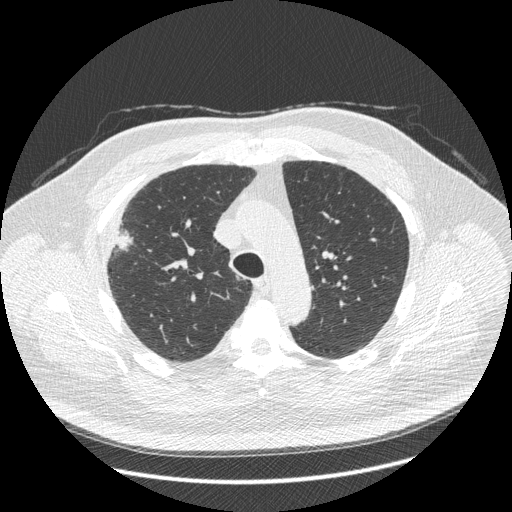
Low-dose screening chest CT, one axial slice. Slice 313 of 426 in the series (ordered by position). 120 kVp. Lung window (W 1500 / L -600 HU). 1.25 mm slice thickness. 512 × 512 image matrix.
Structures marked on this image (manually delineated by an expert):
- lesion 1 (tumor, upper lobe of right lung): bounding box [x1, y1, x2, y2] px = [116, 233, 131, 249]